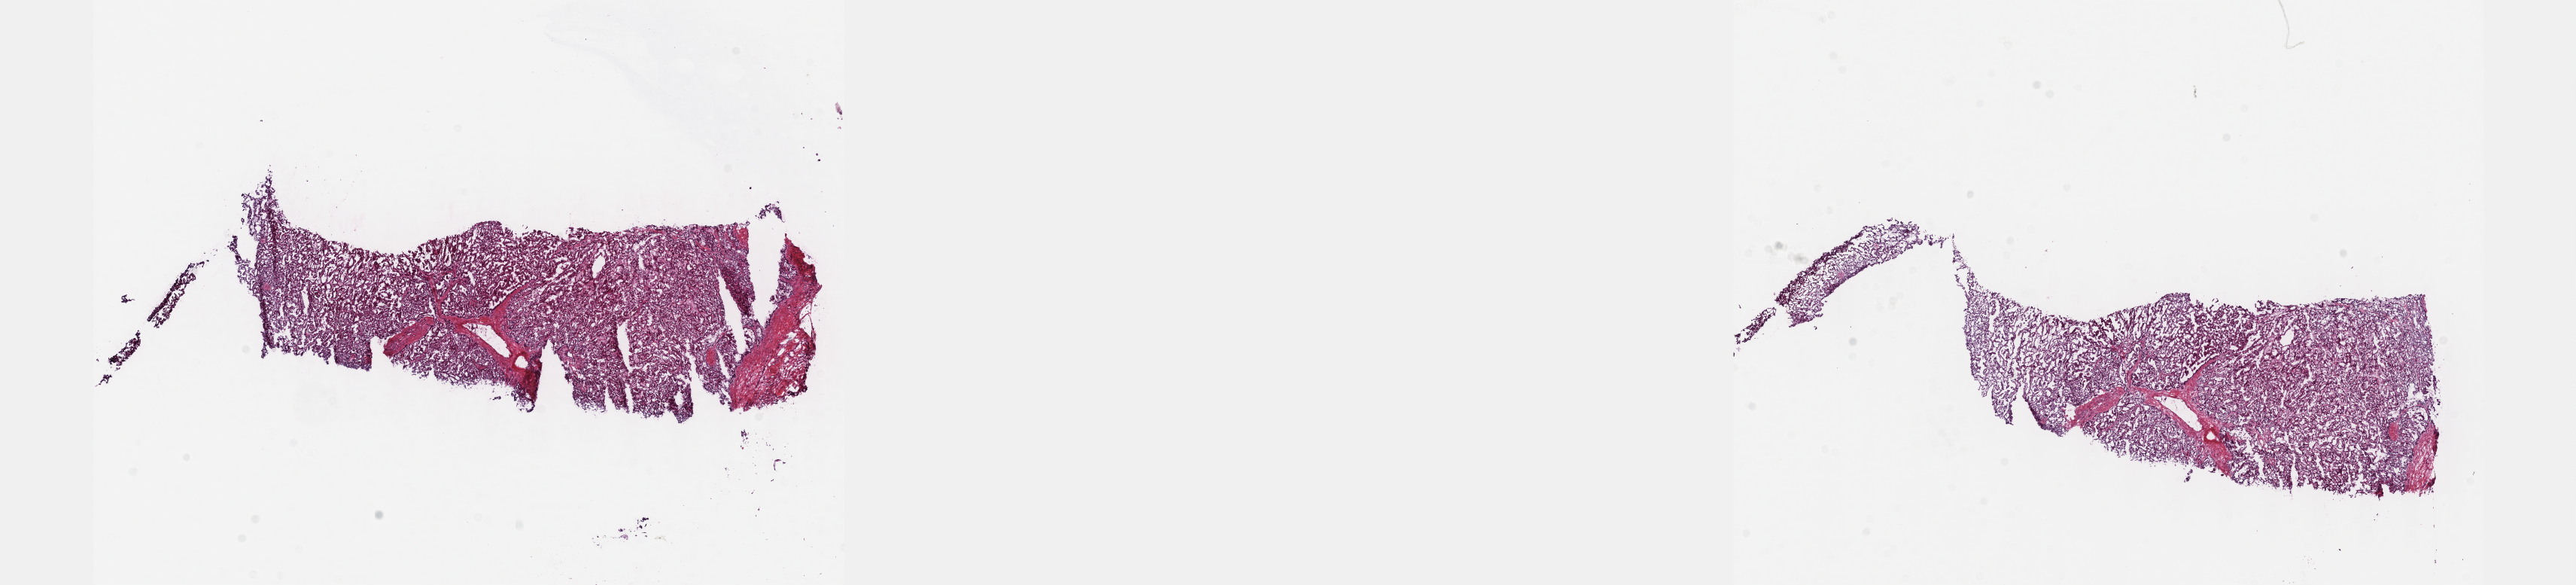
H&E-stained whole-slide image — low-resolution overview of the scanned area, about 27.7 x 6.3 mm. Frozen section from the top of the tissue portion. Primary tumour sample from the kidney. Male, age 67 years at initial diagnosis. Pathologist review of this section (percent, as recorded): tumour cells 85%, tumour nuclei 95%, normal cells 0%, stromal cells 15%, necrosis 0%. Infiltration values recorded for this section: lymphocyte infiltration 0%, monocyte infiltration 0%, neutrophil infiltration 0%.
Histologic diagnosis: Papillary adenocarcinoma, NOS. AJCC pathologic stage: I (7th edition).